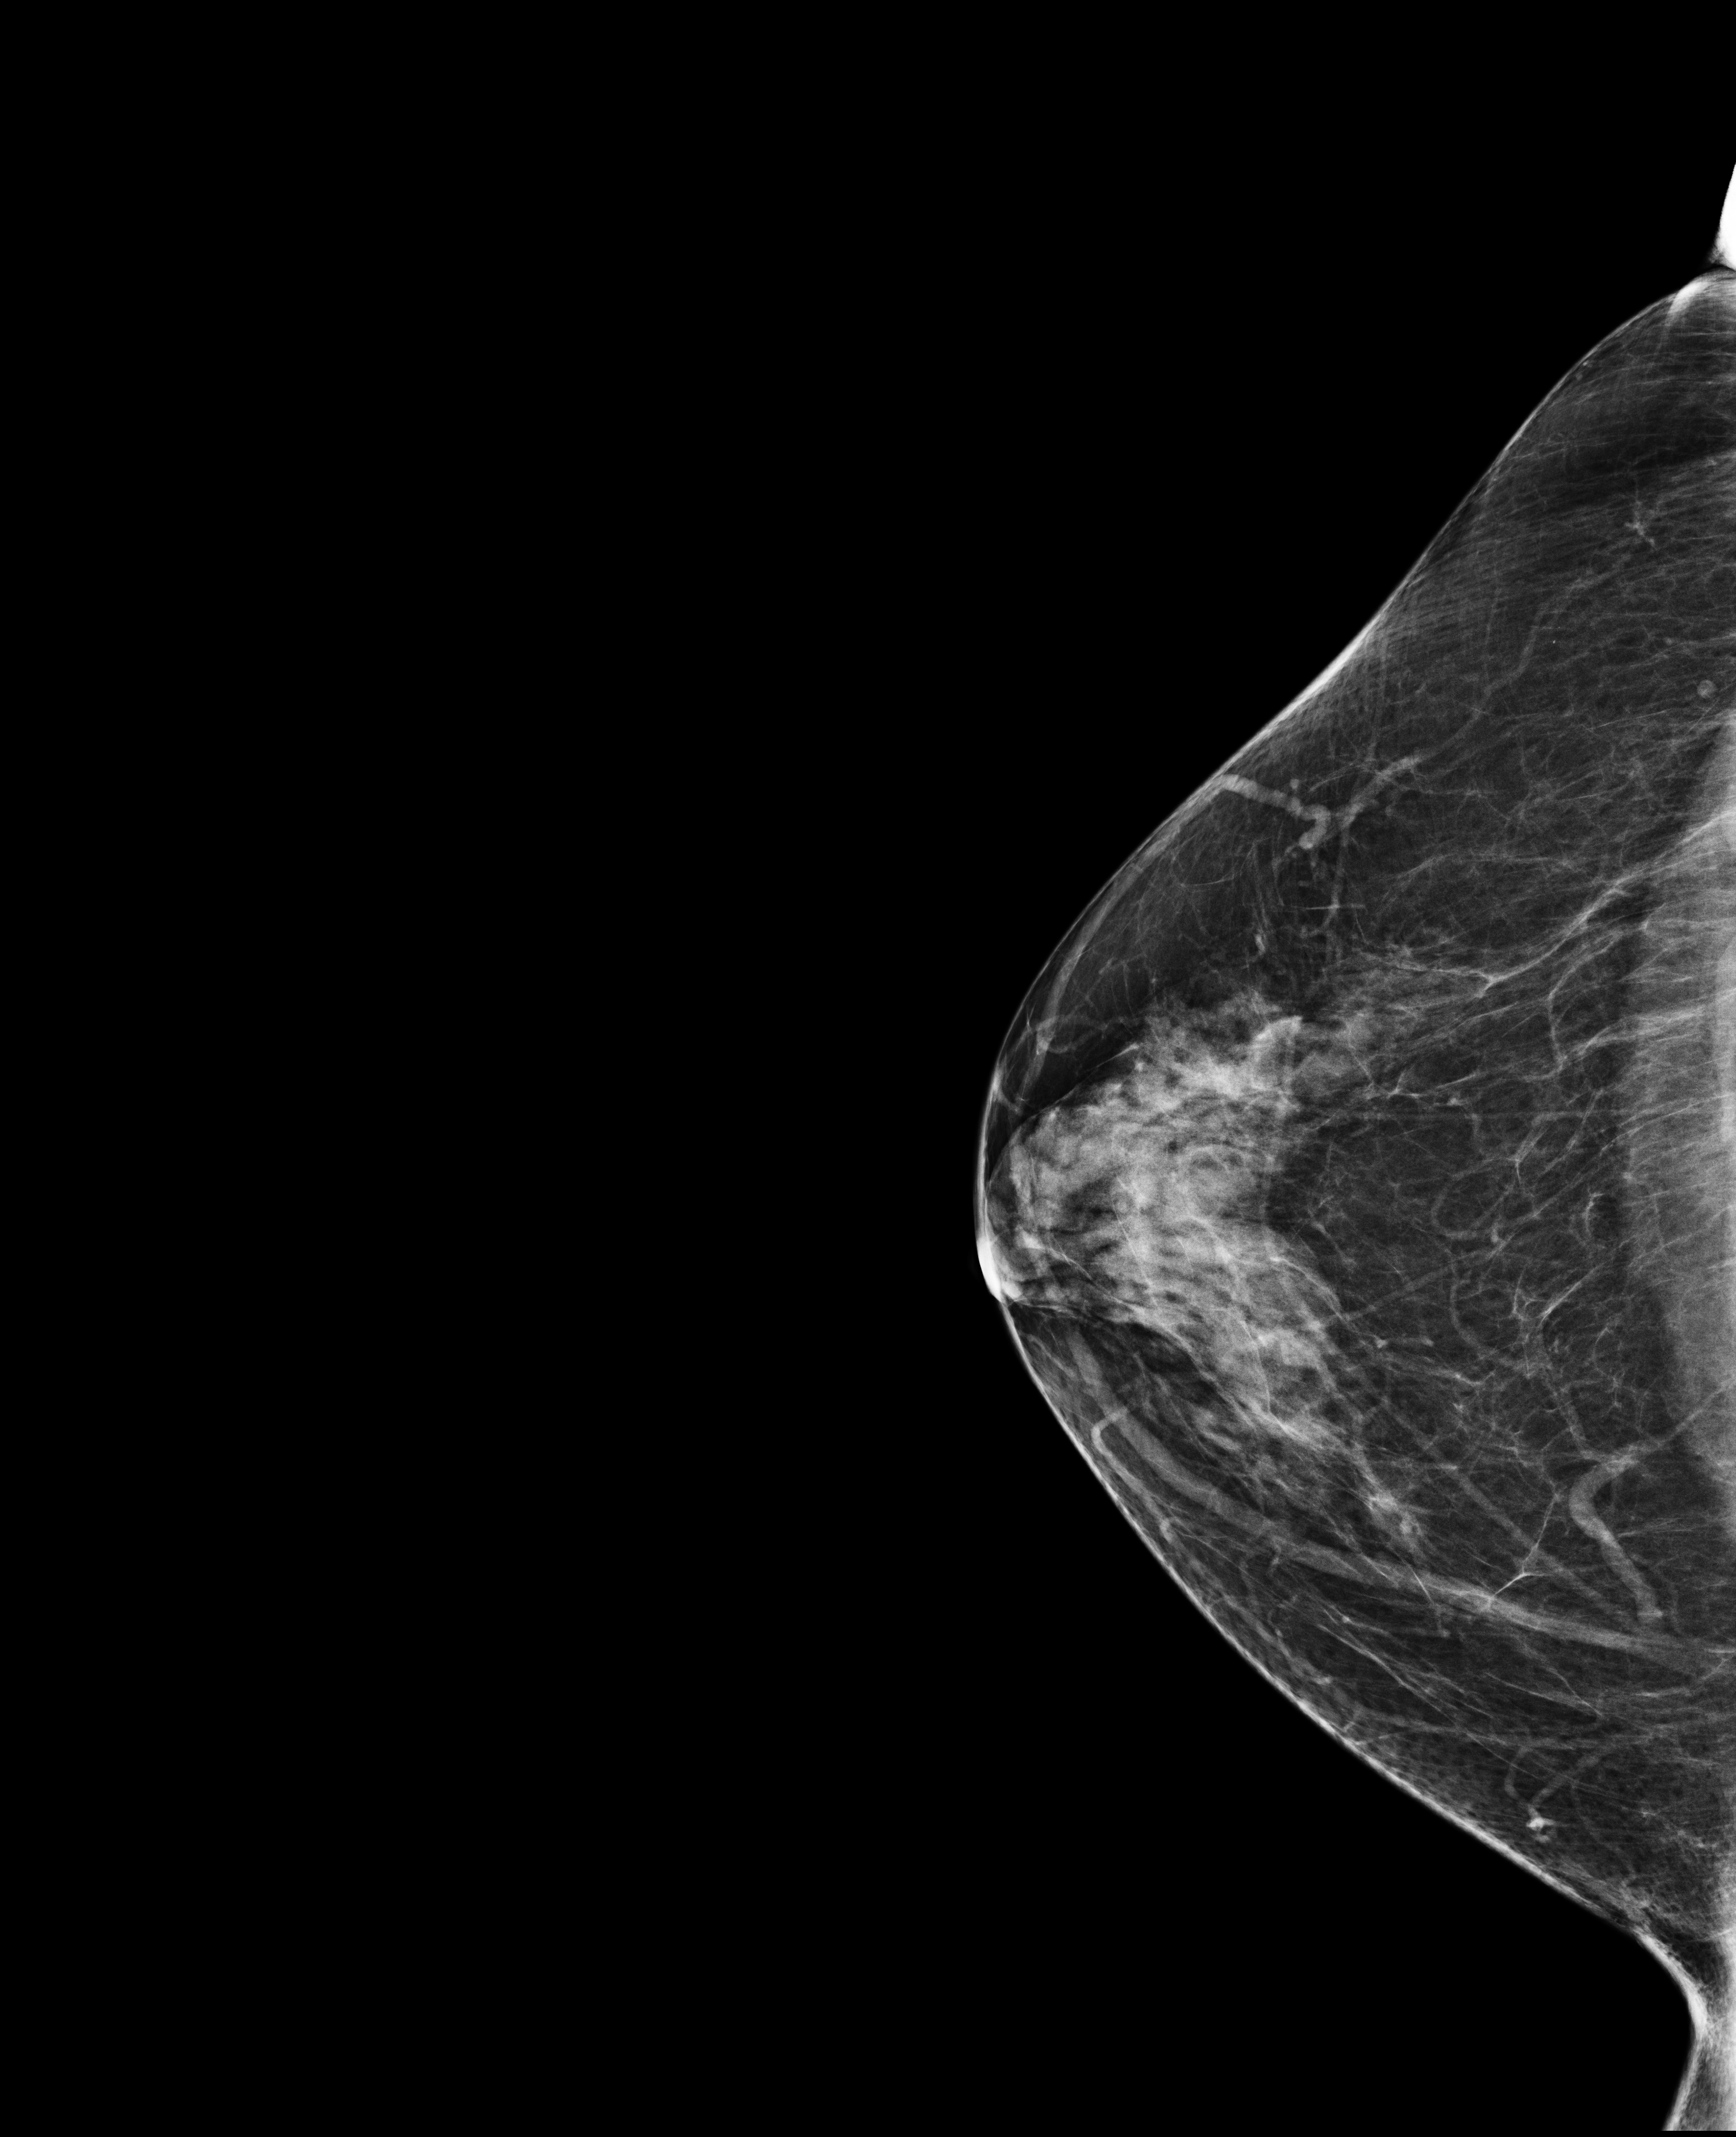
Full-field digital mammogram (FFDM), right breast, craniocaudal (CC) view, screening examination, compressed breast thickness 51 mm. Patient aged 70 years (female).
- BI-RADS breast density category at the screening exam (both breasts, scale 1–4): 3
- final BI-RADS assessment for this screening round (tomosynthesis exam, both breasts): category 1
- recall: no recall after this screen